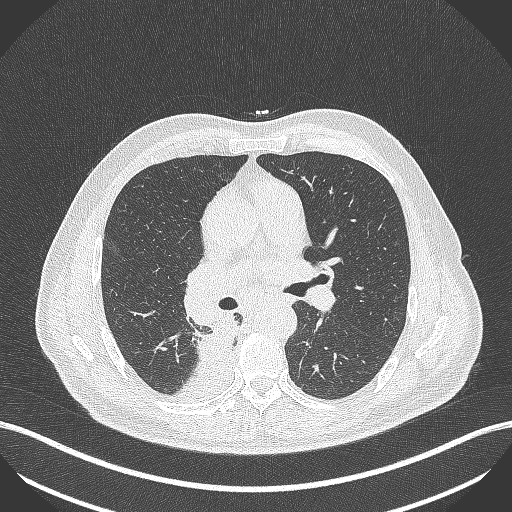
Chest CT, one axial slice. Position 267 of 451 along the scan axis. 100 kVp. Lung window (W 1500 / L -600 HU). 512 × 512 image matrix, field of view 400 × 400 mm. Male patient, age 61 years. From the clinical record (not read from this slice): clinical TNM (as recorded): T1 N0 M0.
Annotated regions visible in this slice (rectangle marked by the reading radiologist):
- lung tumour (recorded histology: small cell carcinoma): box from (x=195, y=318) to (x=244, y=368) px